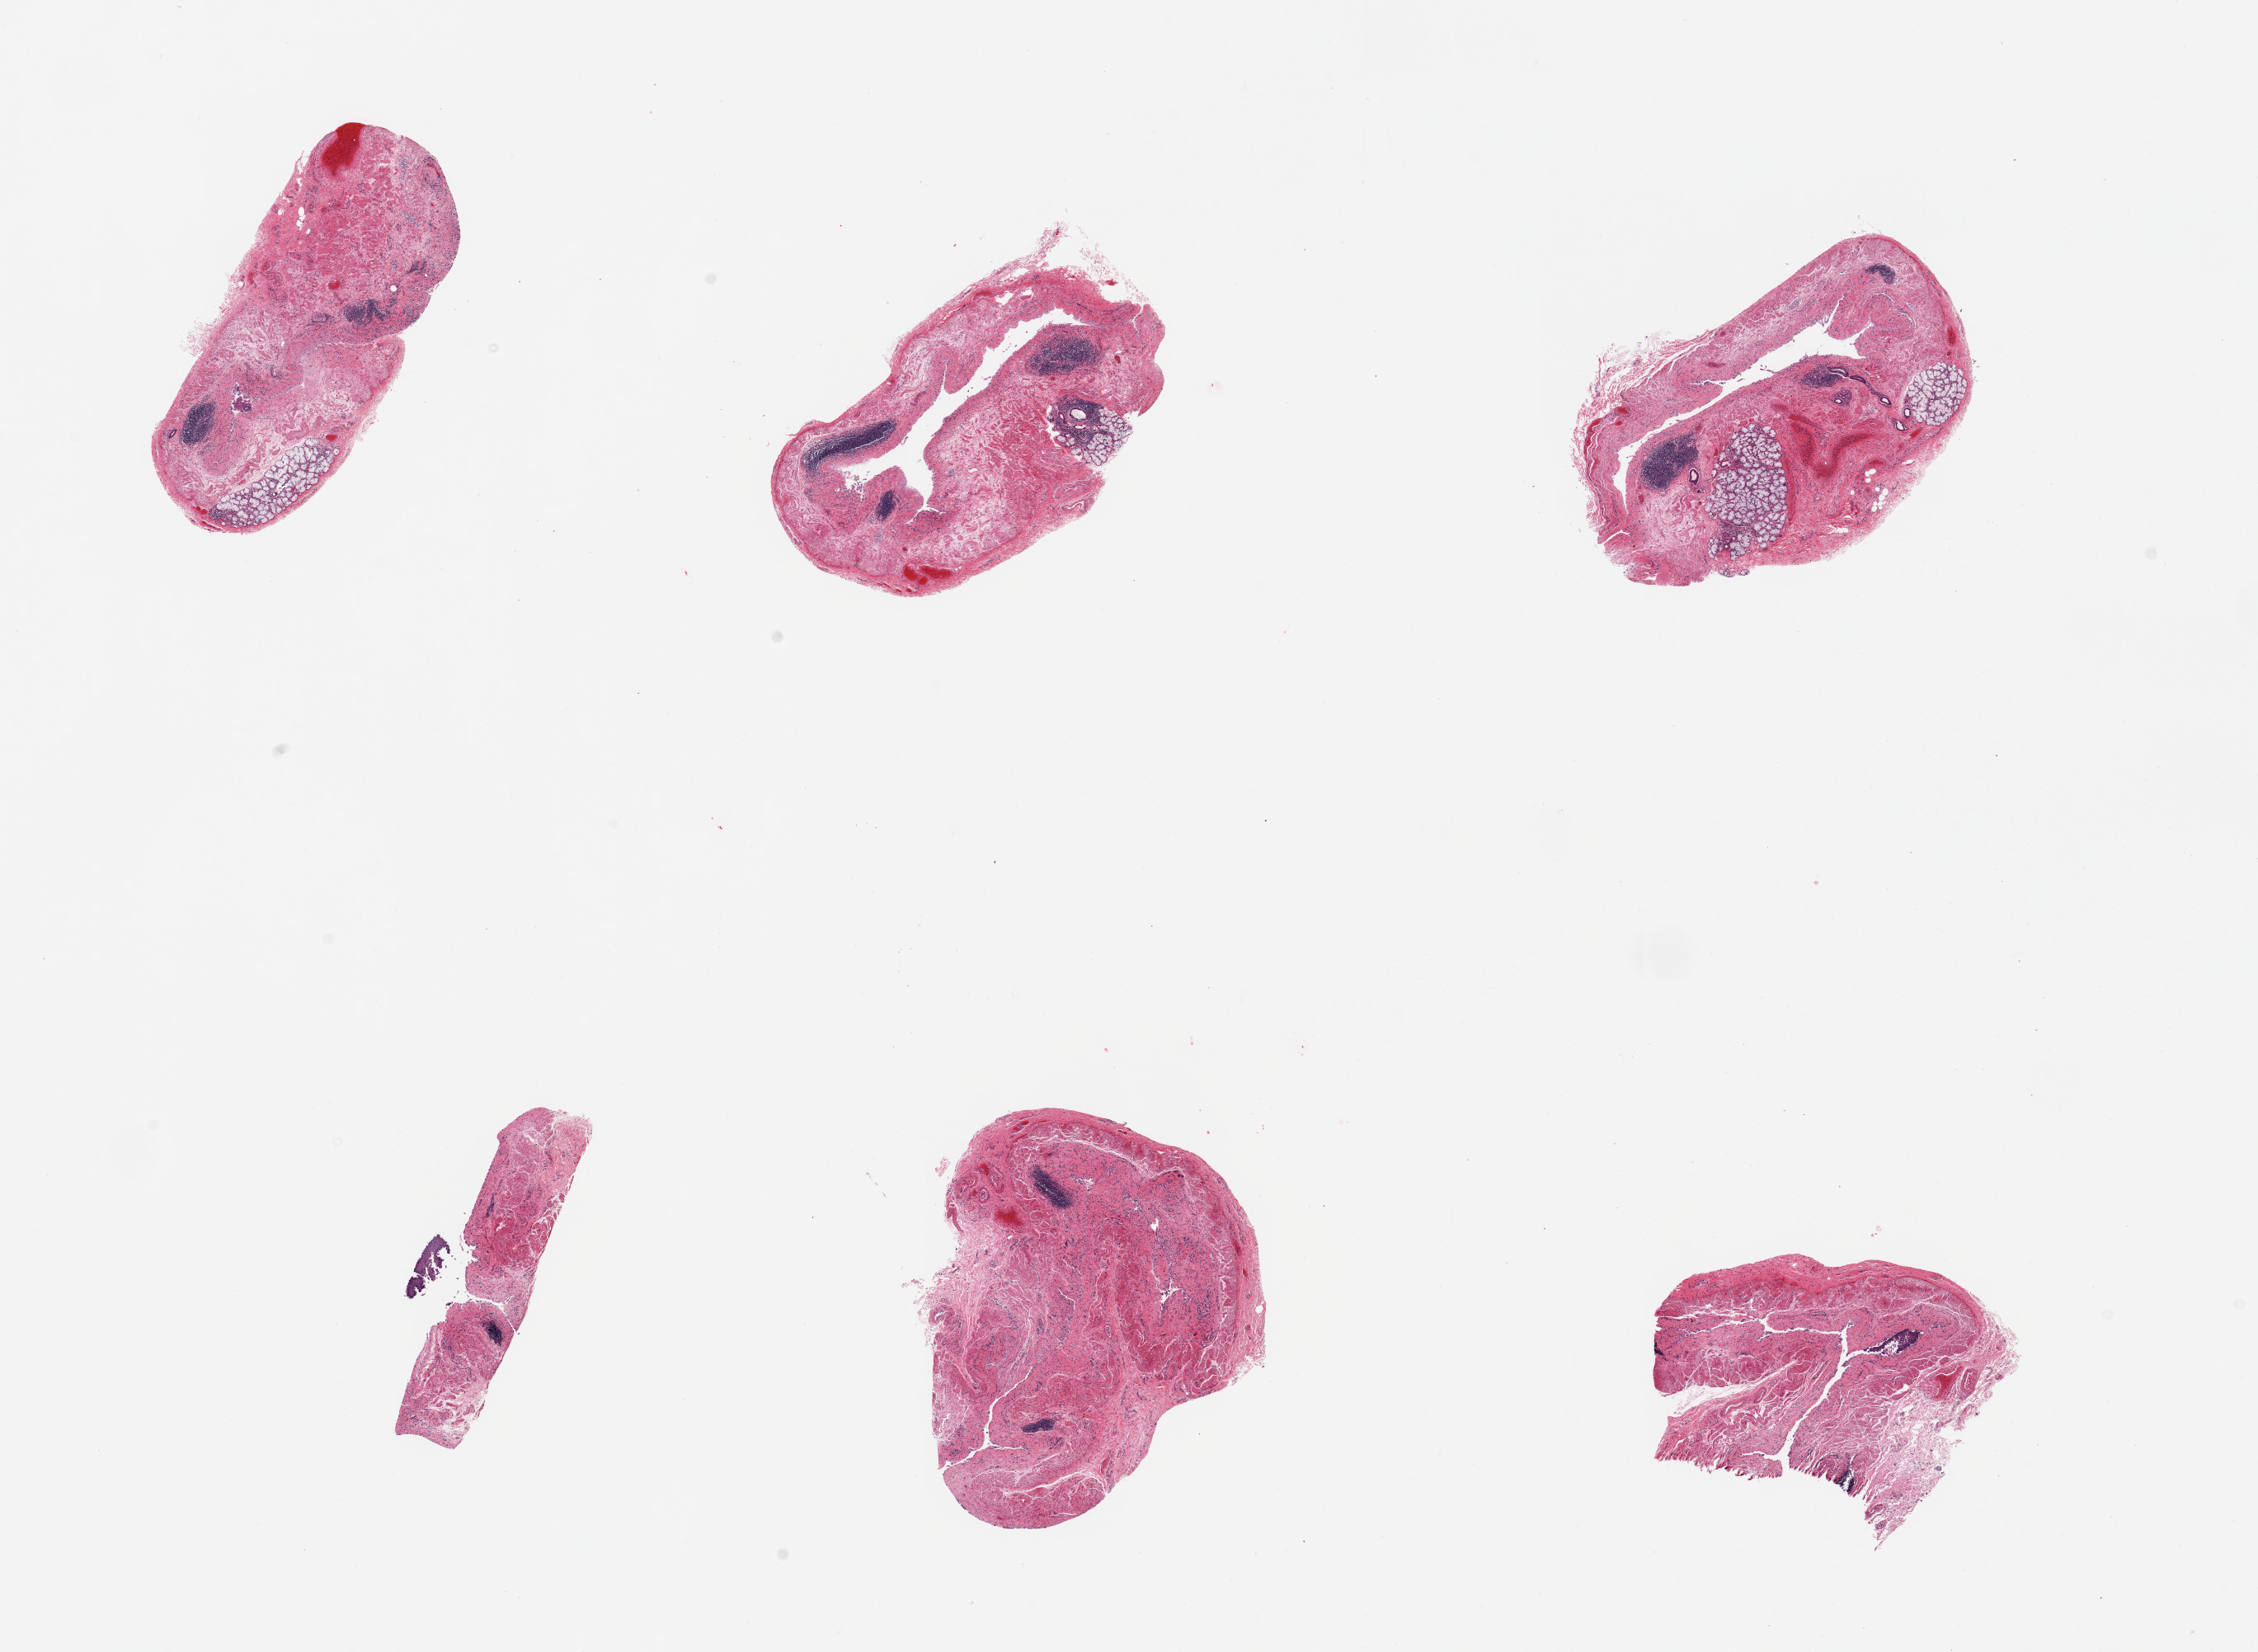
Whole-slide image, haematoxylin and eosin stain — a low-resolution overview of the entire scanned area, about 21.7 x 15.8 mm (from a 20x scan); PAXgene-fixed paraffin-embedded (PFPE) section; section of esophageal mucous membrane (target tissue); tissue donor sample. Donor: male.
Review note (as recorded): 6 pieces; muscularis mucosae, submucosal glands and lymphoid aggregates with only minimal squamous epithelium present.